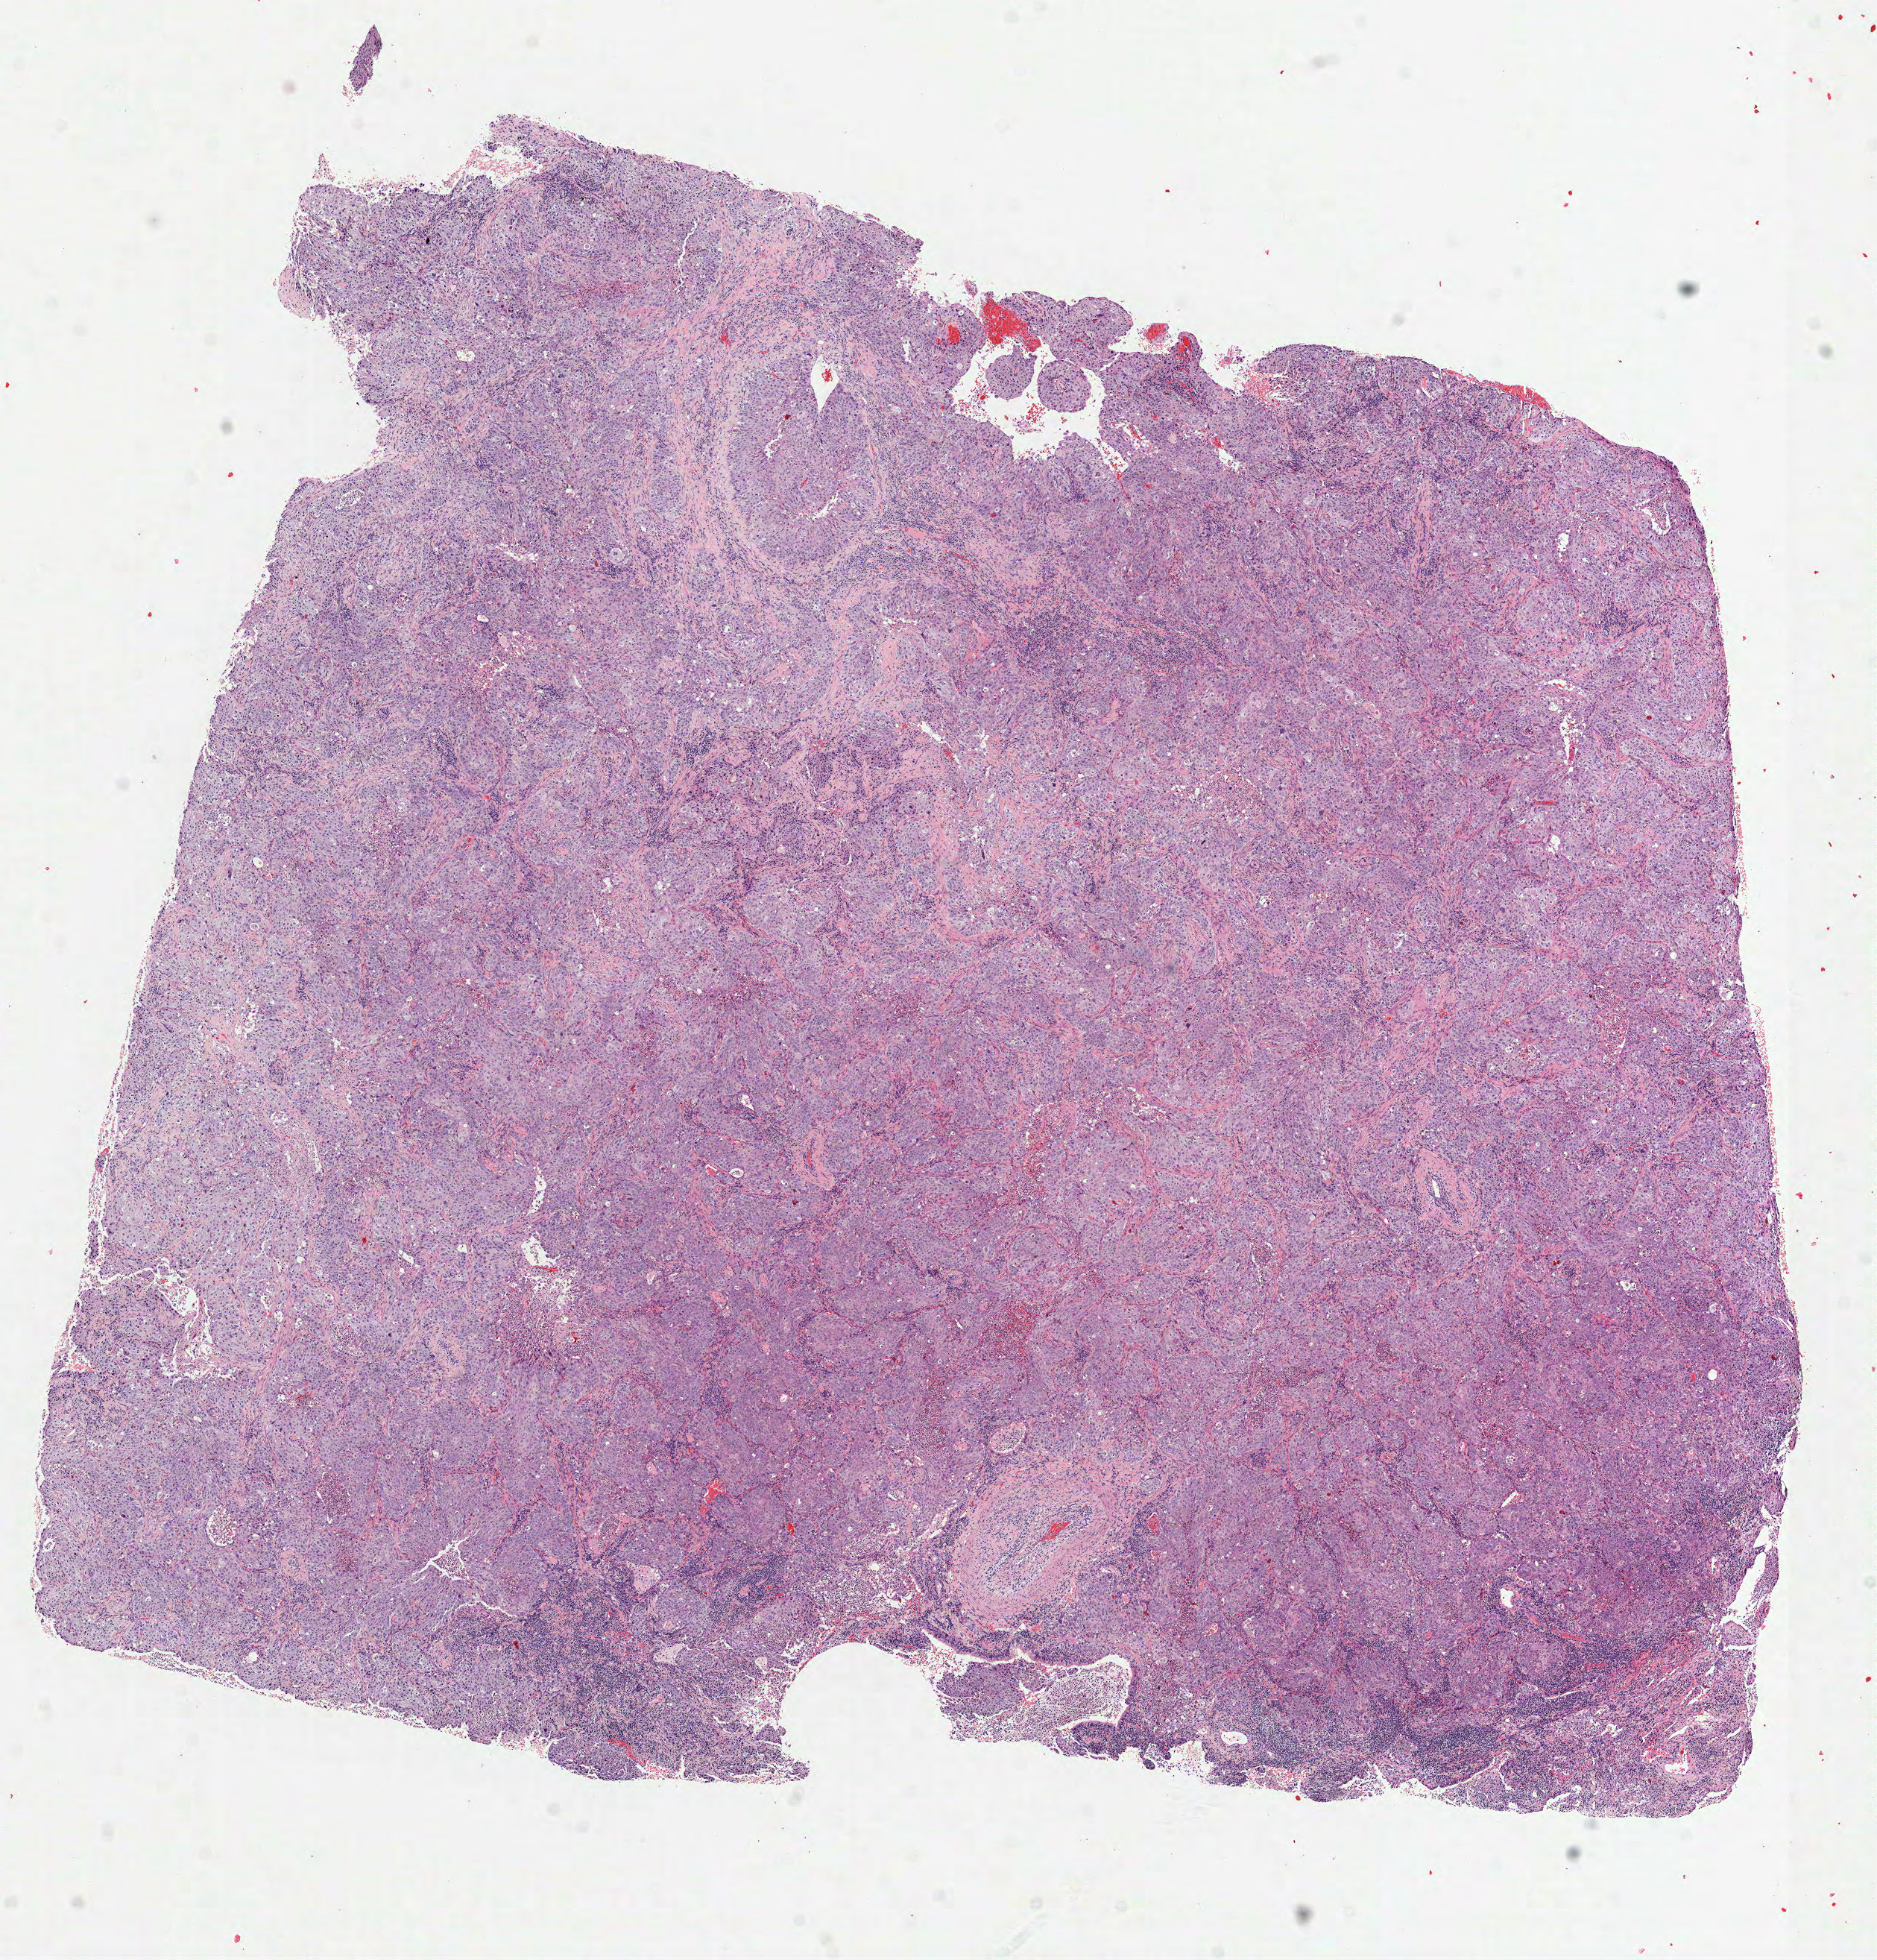
Digitized Hematoxylin and eosin (H&E) stained tissue section (whole slide), a low-resolution overview of the entire scanned area, about 10.2 x 10.6 mm, frozen section, primary tumour sample from the lung. Patient: male, age at initial diagnosis 71 years. Slide review estimates, as recorded: tumour cells 88%, tumour nuclei 75%, normal cells 0%, stromal cells 10%, necrosis 2%.
Laterality: right. Pathologic diagnosis: Squamous cell carcinoma, NOS (lower lobe, lung). AJCC pathologic stage: IIB.